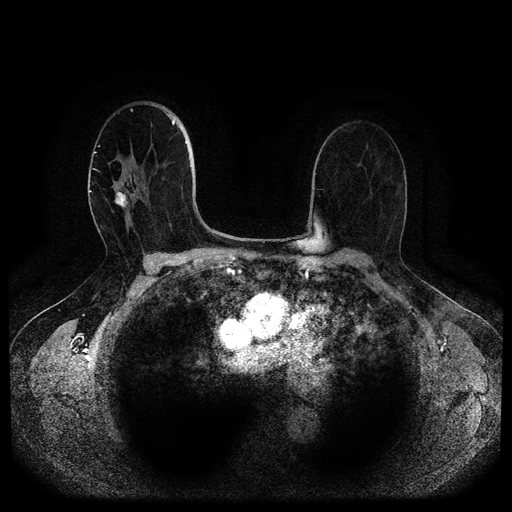
Breast MRI (dynamic contrast-enhanced, multi-phase), one axial slice; position 64 of 116 along the scan axis; dynamic contrast-enhanced series, time point 2 of 5 at this slice position (early post-contrast); 1.5 T; TE 2.6 ms, TR 5.3 ms; 2 mm slice thickness; 512 × 512 image matrix, field of view 350 × 350 mm. Patient: female, 82 years.
Outlined on this slice (semi-automatically segmented with operator editing):
- breast lesion (labelled 'tumour' in the annotation; benign lesions carry a separate 'benign' label): bounding box (x1, y1, x2, y2) in pixels: (114, 190, 129, 208)